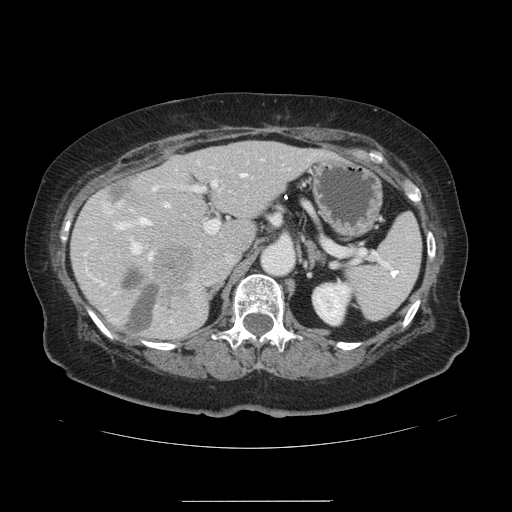
Contrast-enhanced abdominal CT, one axial slice; slice 80 of 141 in the series (ordered by position); intravenous contrast given; soft-tissue window (W 400 / L 40 HU); 2.5 mm slice thickness; 512 × 512 image matrix, field of view 393 × 393 mm. Female patient, age 74 years. From the clinical record (not read from this slice): diagnosis: colorectal cancer liver metastases, imaged before liver resection; multiple liver metastases: yes; largest metastasis: 7 cm; disease in both lobes: yes.
Annotated regions visible in this slice (outlined manually by an expert reader):
- hepatic veins: bounding box (x1, y1, x2, y2) in pixels: (119, 173, 245, 228)
- liver: (73, 142, 325, 341)
- planned liver remnant (the part of the liver to remain after resection): (75, 142, 325, 340)
- portal vein (with intrahepatic branches): (131, 180, 219, 259)
- liver metastasis: (103, 179, 143, 208)
- liver metastasis: (123, 271, 160, 334)
- liver metastasis: (155, 245, 194, 305)